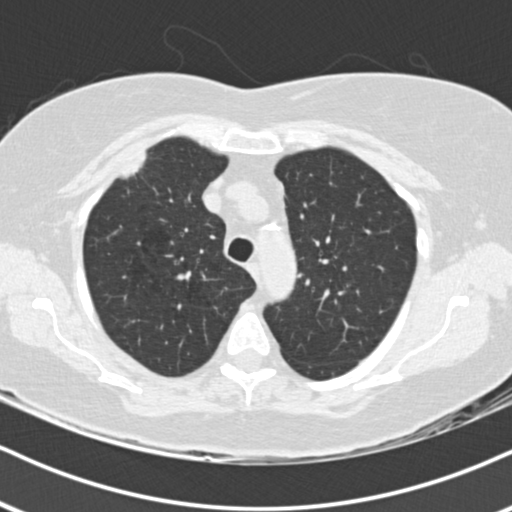
Low-dose screening chest CT, one axial slice. Slice 139 of 178 in the series (ordered by position). Reconstruction kernel B30f. Lung window (W 1500 / L -600 HU). 2 mm slice thickness. 512 × 512 image matrix, field of view 320 × 320 mm.
Structures marked on this image (outlined manually by an expert reader):
- lesion 1 (tumor, upper lobe of right lung): box from (x=119, y=151) to (x=147, y=179) px